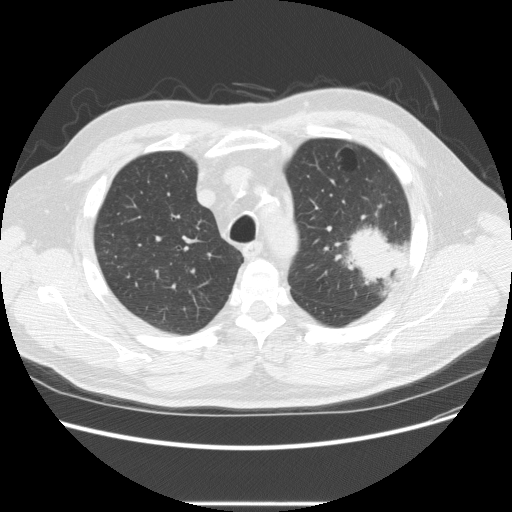
Low-dose screening chest CT, axial slice; baseline annual screen; lung window (W 1500 / L -600 HU); 2.5 mm slice thickness; standard (soft-tissue) reconstruction kernel (STANDARD). Male, age 73 years at enrolment.
Expert-annotated lung lesion, box from (x=332, y=215) to (x=414, y=285) px. The screening reader recorded 2 non-calcified nodules or masses ≥4 mm on this exam; which of them this box marks is not recorded. Official screen result: positive, change unspecified: nodule(s) >= 4 mm or enlarging nodule(s), mass(es), or other non-specific abnormalities suspicious for lung cancer. Participant outcome: lung cancer diagnosed 11 days after this screen — bronchiolo-alveolar adenocarcinoma, NOS, other location, well differentiated (G1), stage IV (AJCC 6th edition).